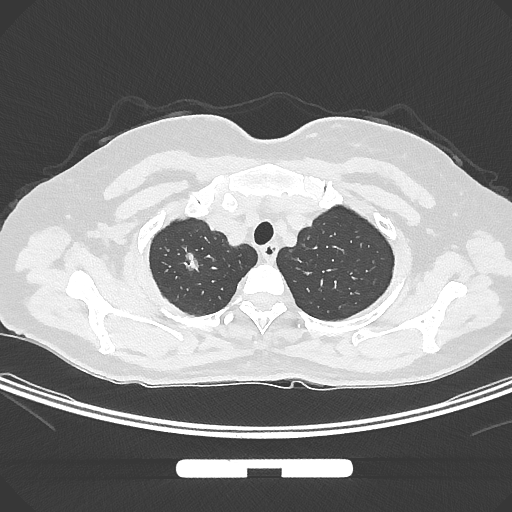
Chest CT, one axial slice. Position 257 of 294 along the scan axis. Reconstruction kernel IMR1,SharpPlus. Lung window (W 1500 / L -600 HU). 1 mm slice thickness. 512 × 512 image matrix, field of view 369 × 369 mm. Female patient, age 58 years. From the clinical record (not read from this slice): clinical TNM (as recorded): T1b N0 M0; histopathological grade: G2-3.
Annotated regions visible in this slice (bounding box drawn by a radiologist):
- lung tumour (recorded histology: adenocarcinoma): bounding box [x1, y1, x2, y2] px = [175, 242, 208, 280]